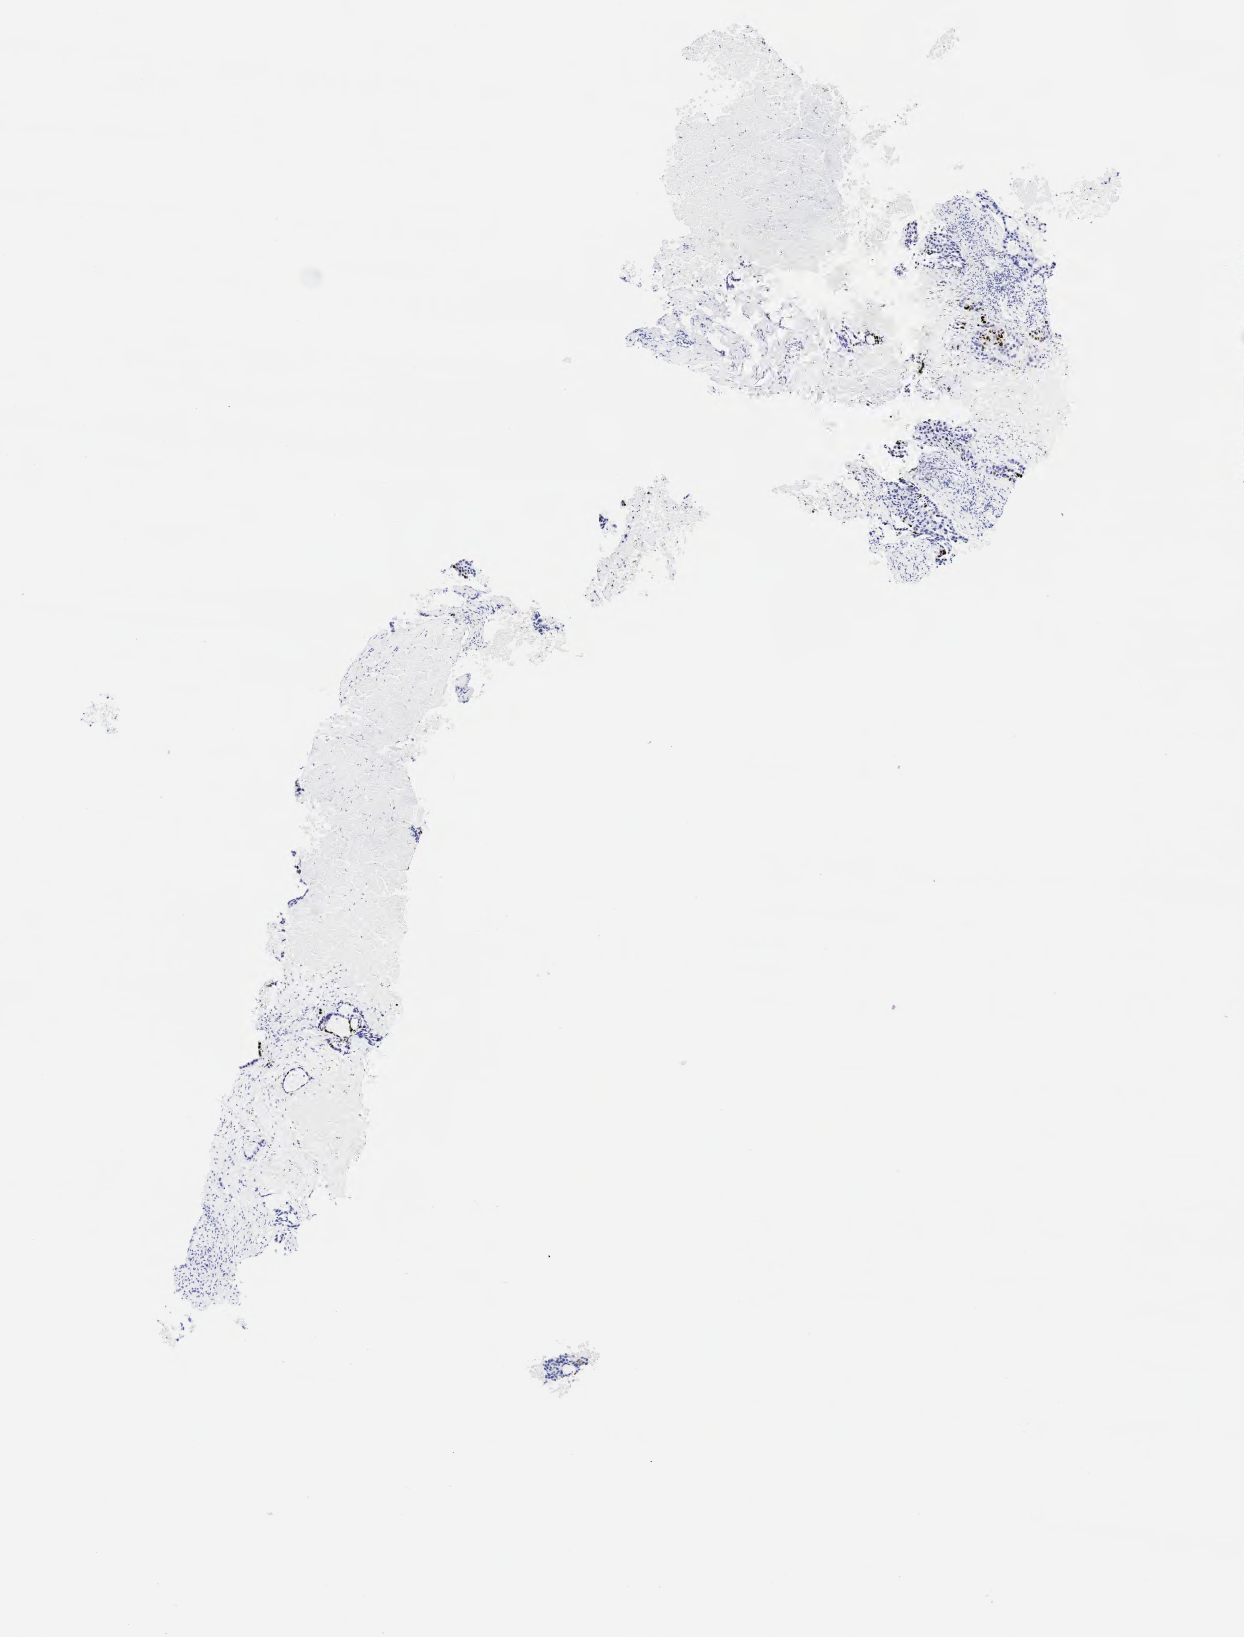
Immunohistochemistry (IHC) whole-slide image stained for p40, low-resolution overview of the scanned area, about 5.0 x 6.6 mm; specimen: tumor tissue; anatomic site: lung (right). Male patient, age 66 years.
- diagnosis: Adenocarcinoma, NOS